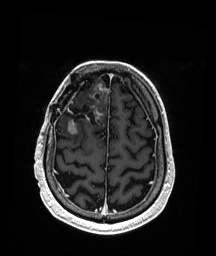
Brain MRI from a brain-tumour surgery series, one axial slice. Position 49 of 192 along the scan axis. T1-weighted post-contrast. 1 mm slice thickness. 216 × 256 image matrix. From the clinical record (not read from this slice): histopathology: Astrocytoma; WHO grade: 3; IDH mutation: yes.
Annotated regions visible in this slice (expert manual segmentation):
- previous resection cavity: bounding box <65,93,101,126> (left, top, right, bottom; pixels)
- tumour: <68,85,109,134>